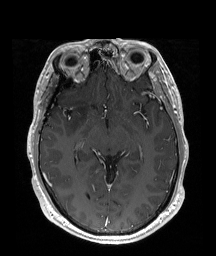
Brain MRI from a brain-tumour surgery series, one axial slice; position 112 of 192 along the scan axis; T1-weighted post-contrast; 216 × 256 image matrix, field of view 219 × 260 mm. Case-level facts recorded for this patient, not image findings: histopathology: Astrocytoma; WHO grade: 2; IDH mutation: yes; tumour location: Right Insular.
Structures marked on this image (manually delineated by an expert):
- tumour: bounding box <68,96,91,135> (left, top, right, bottom; pixels)